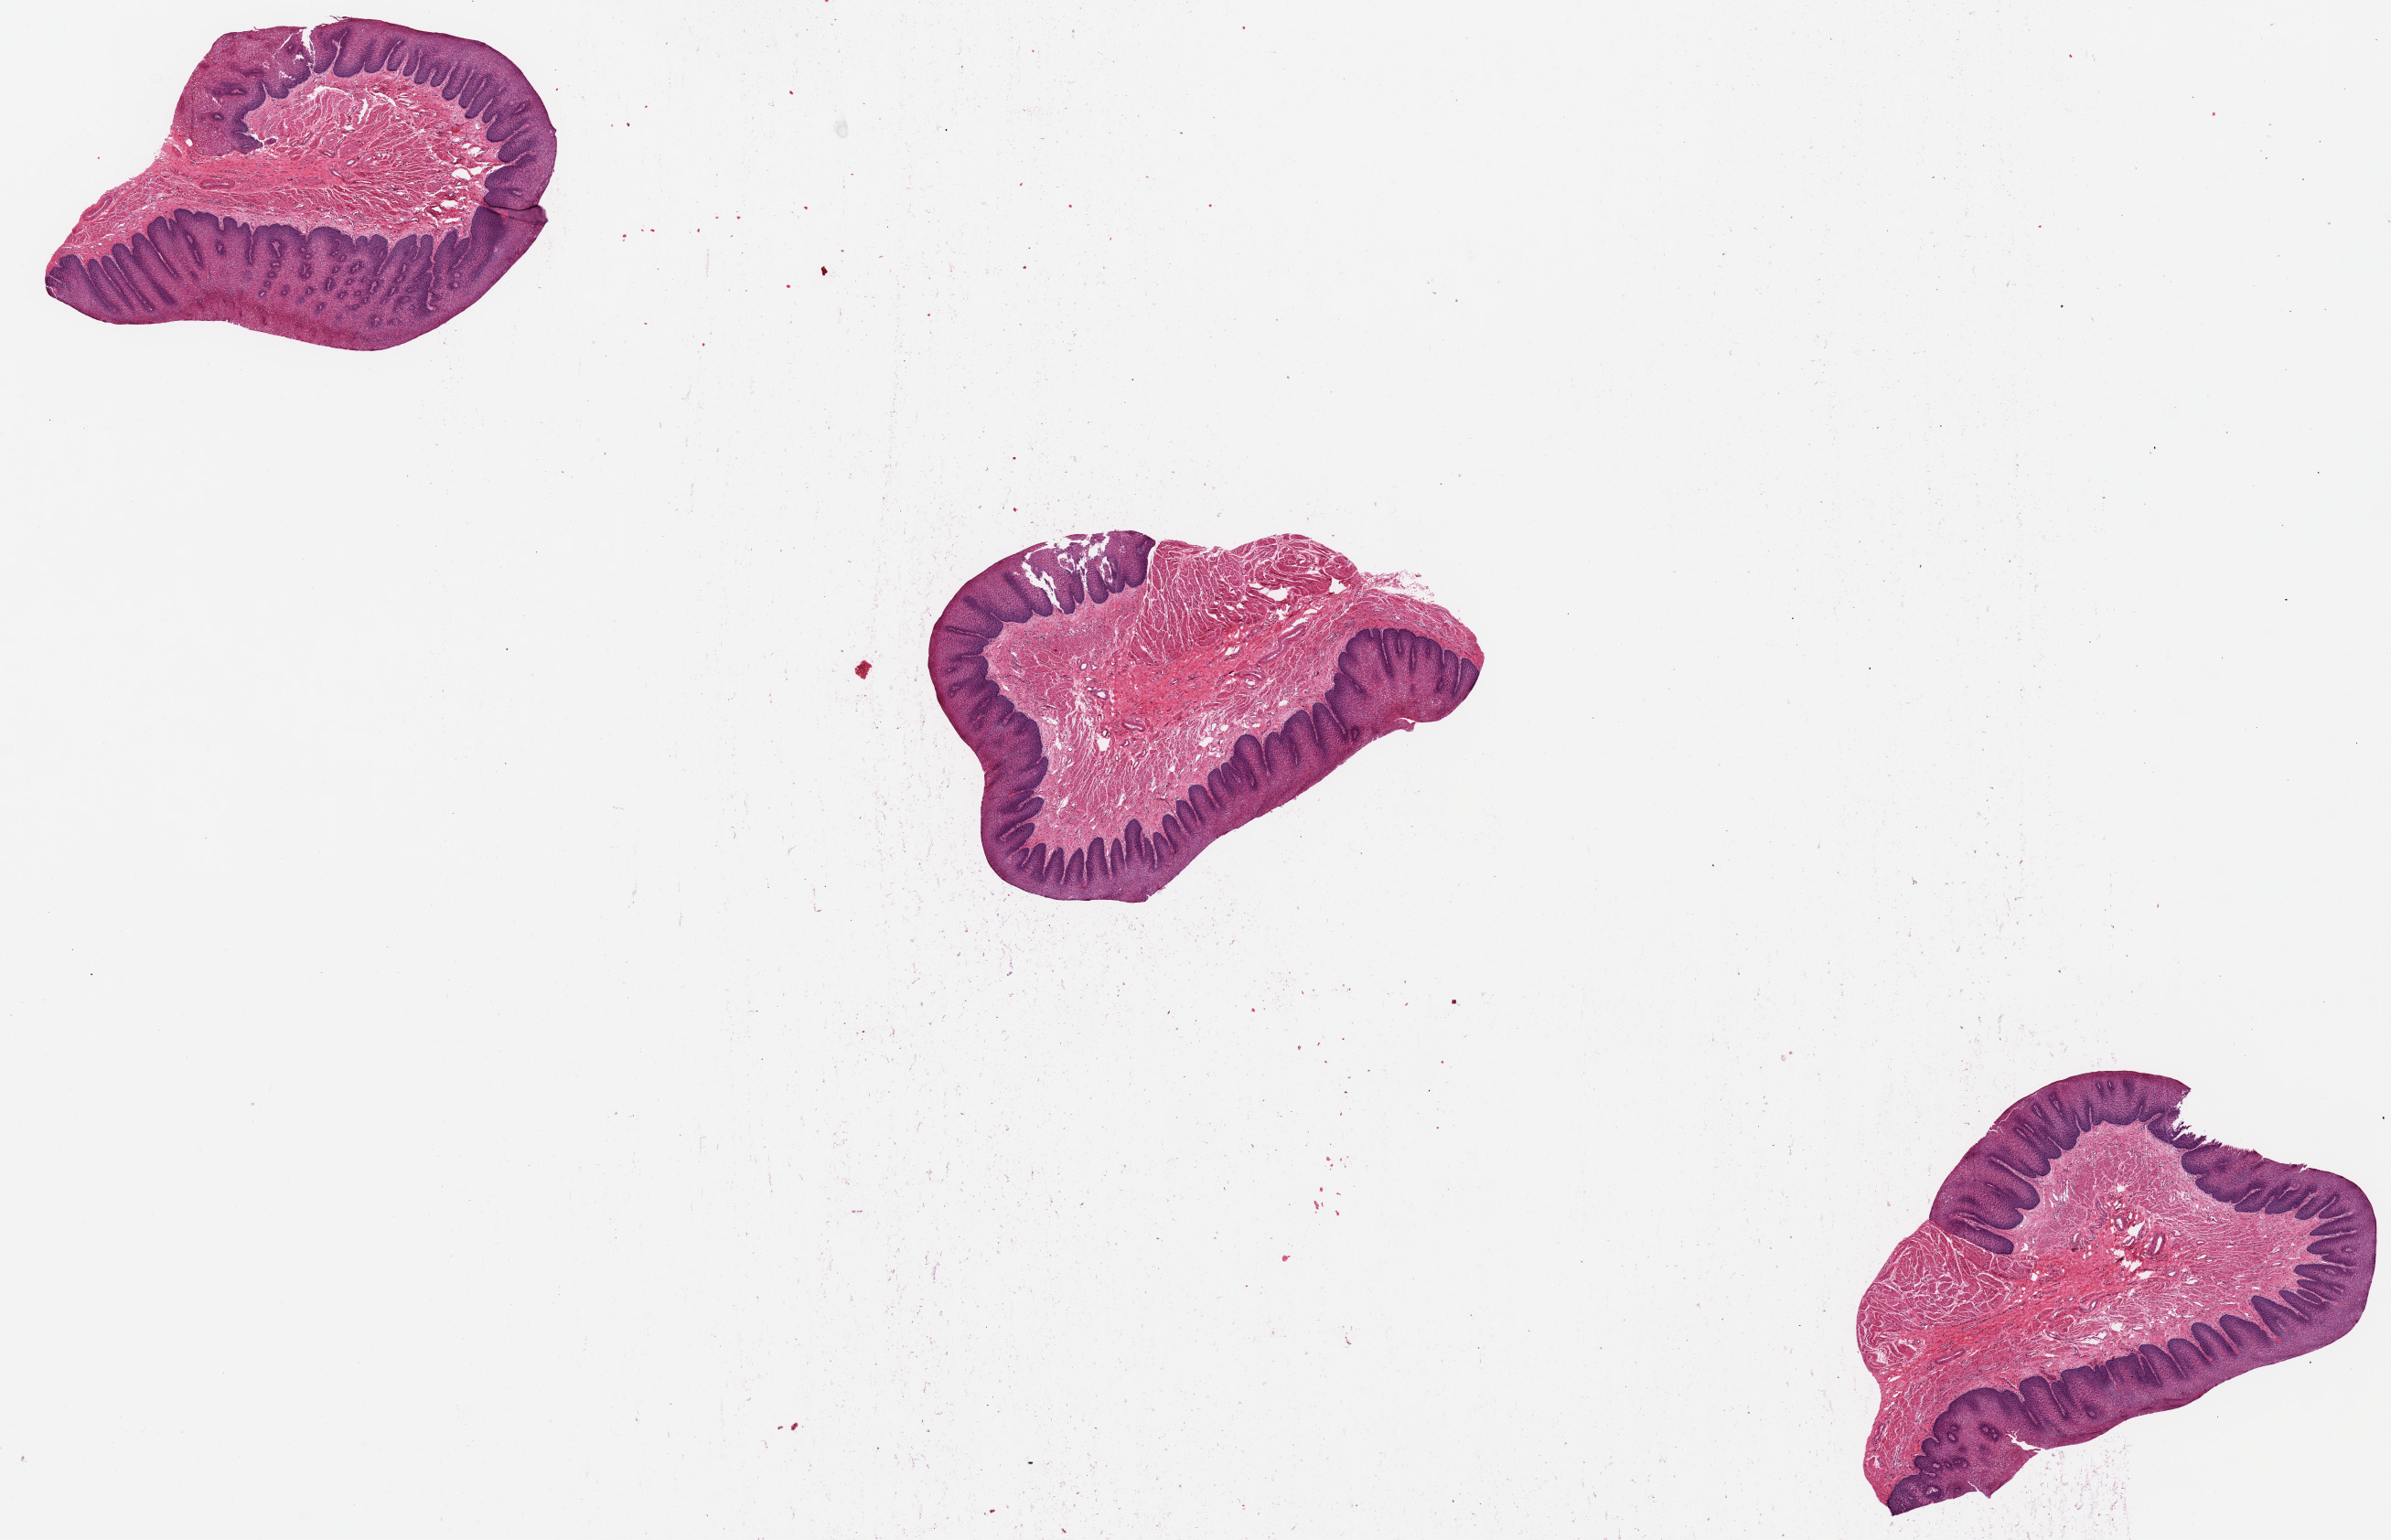
Whole-slide image, H&E stain — shown as a low-resolution overview of the whole scanned area (about 20.7 x 13.3 mm, acquisition: 20x scan), PAXgene-fixed paraffin-embedded (PFPE) section, sampled site (target tissue): esophageal mucous membrane, donor tissue sample.
- pathologist's review note for this sample: 3 pieces; prominent muscularis mucosae